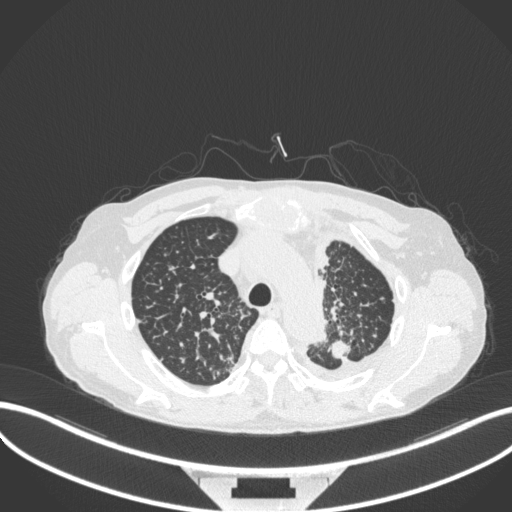
Chest CT, one axial slice. Slice 272 of 319 in the series (ordered by position). Reconstruction kernel B31f. Lung window (W 1500 / L -600 HU). 1 mm slice thickness. 512 × 512 image matrix, field of view 400 × 400 mm. Male patient, age 58 years. Case-level facts recorded for this patient, not image findings: clinical TNM (as recorded): T1c N3 M1.
Annotated regions visible in this slice (rectangle marked by the reading radiologist):
- lung tumour (recorded histology: adenocarcinoma): bounding box [x1, y1, x2, y2] px = [326, 339, 351, 362]